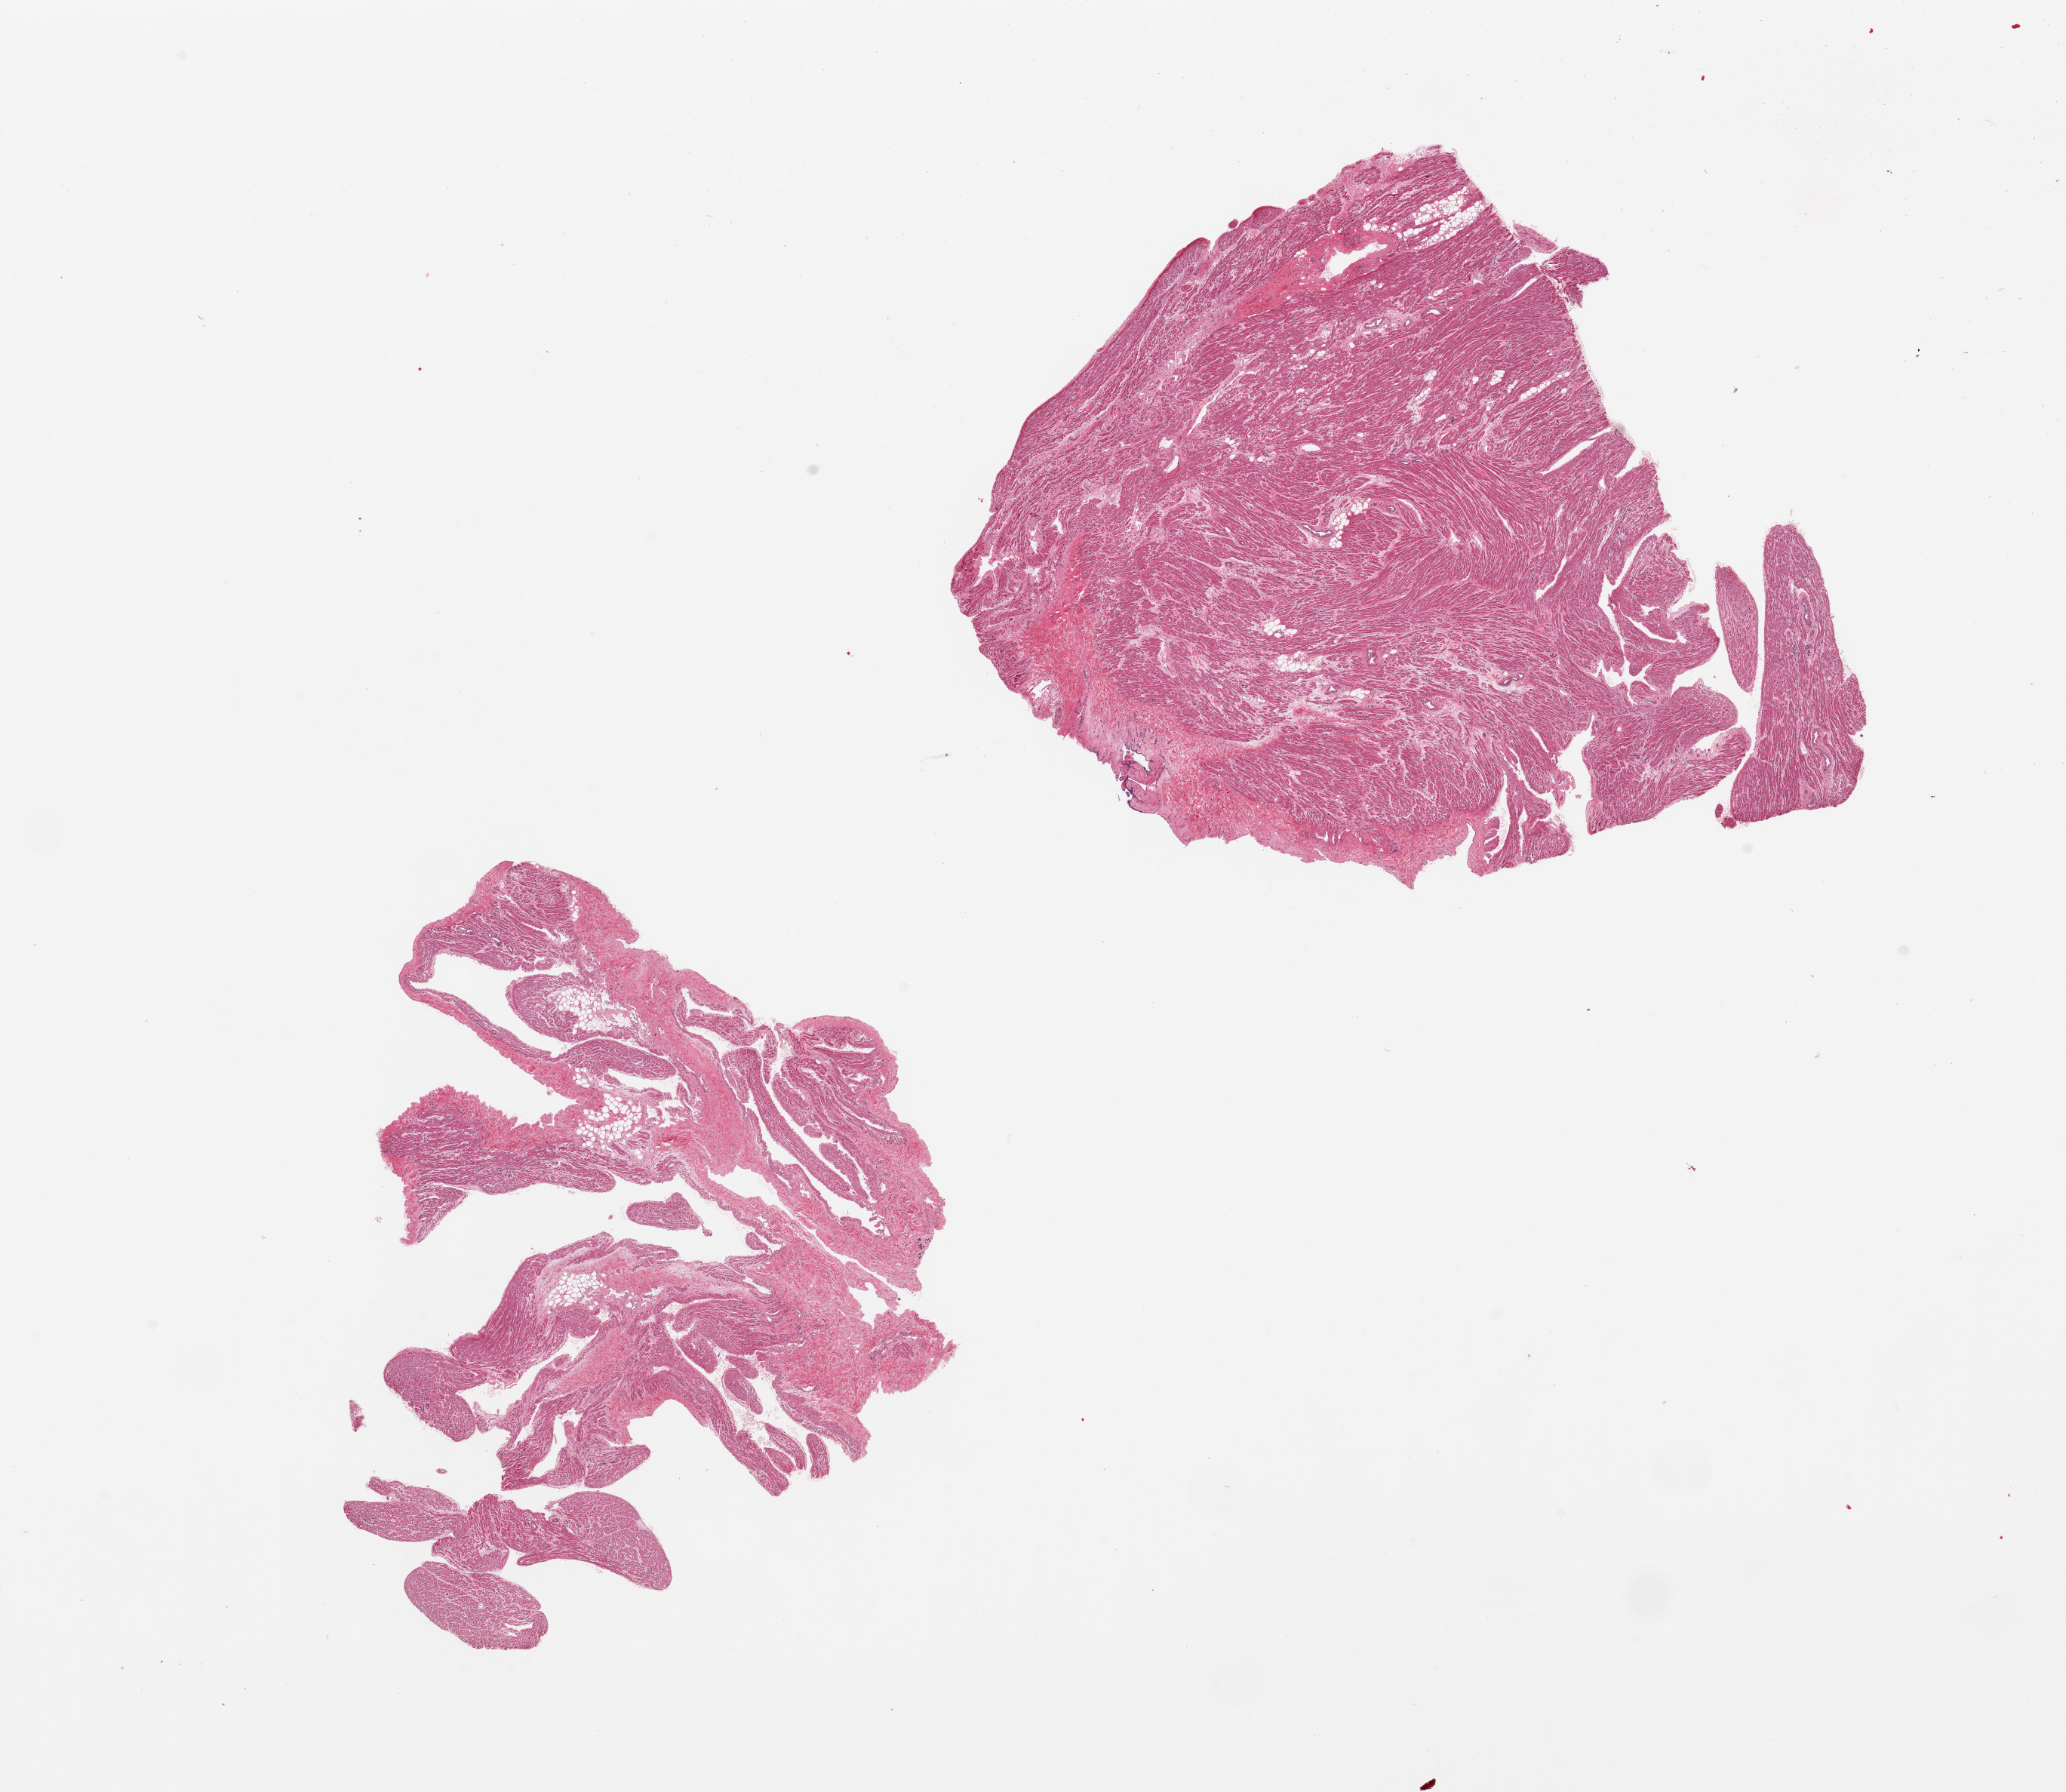
Haematoxylin and eosin whole-slide image, brightfield — a low-resolution overview of the entire scanned area, about 21.7 x 18.8 mm (slide scanned at 20x), PAXgene-fixed, paraffin-embedded tissue, target tissue: auricular appendage, tissue donor sample. Donor sex: female.
Review note (as recorded): 2 pieces; no abnormalities.